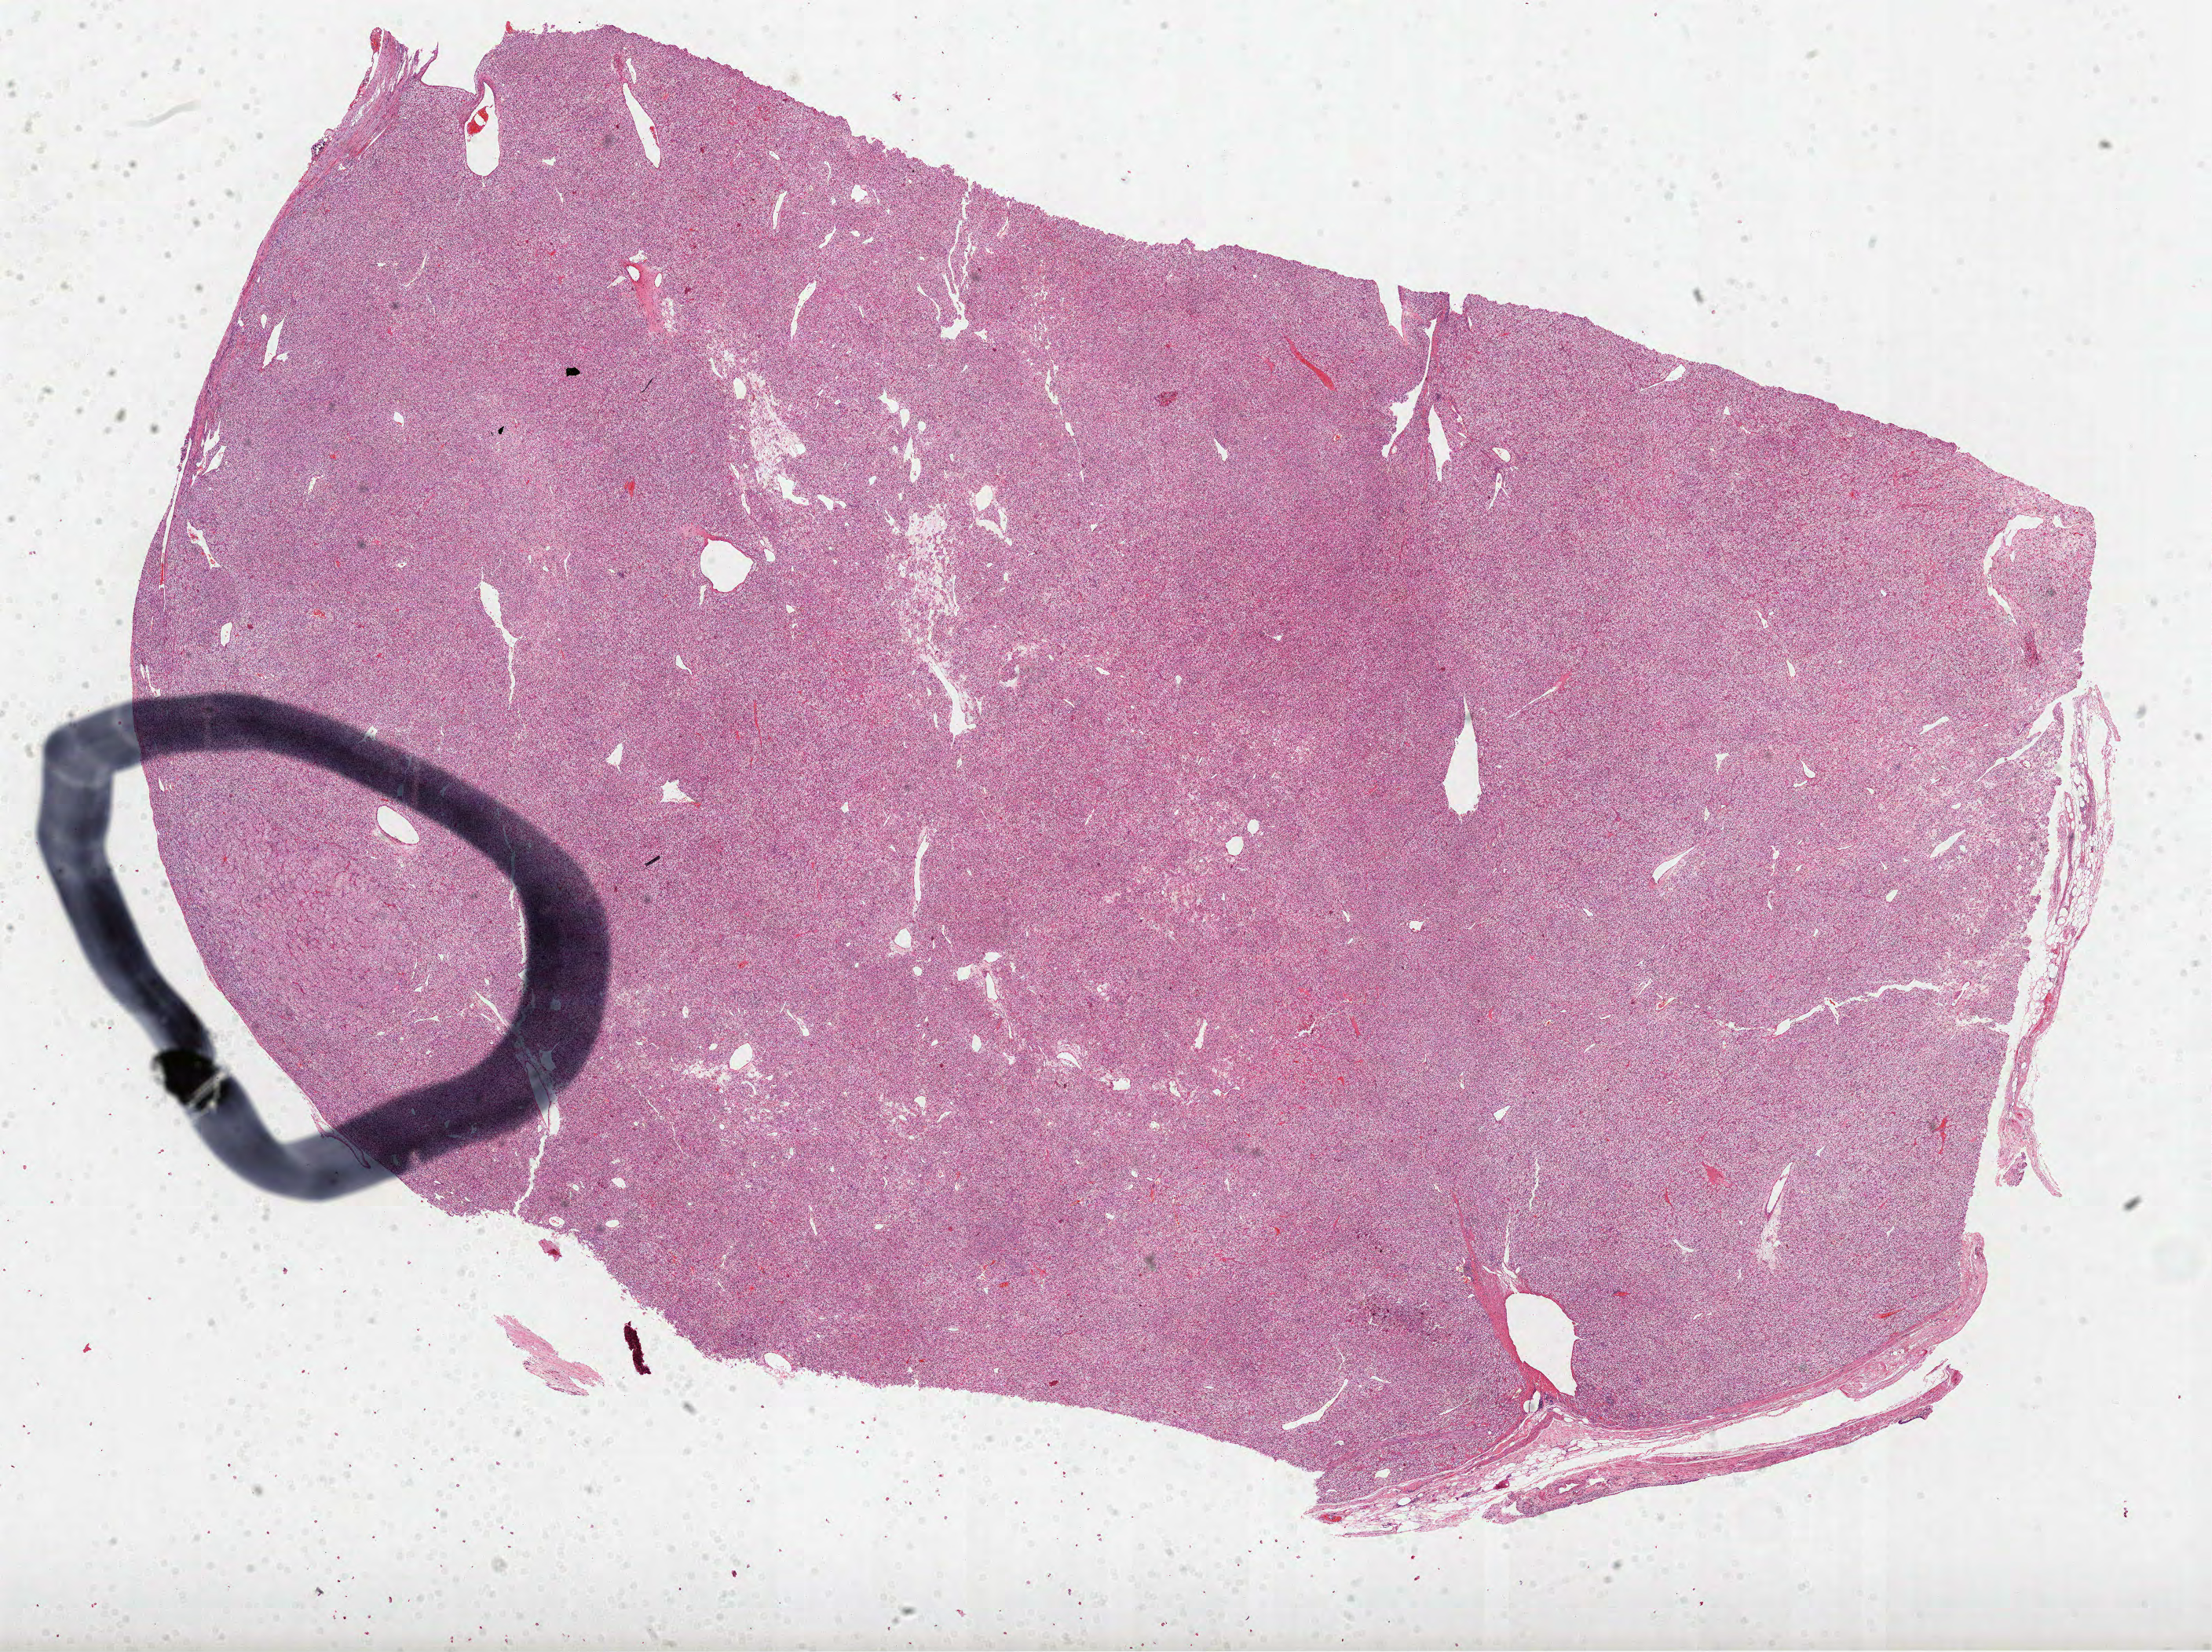
Whole-slide histology image, H&E, whole scanned area (about 22.7 x 17.0 mm, acquisition: 40x scan) shown as a low-resolution overview; formalin-fixed paraffin-embedded (FFPE) diagnostic section; kidney, primary tumour sample. Male, age 81 years at initial diagnosis. Histologic grade: G3 (poorly differentiated).
AJCC pathologic stage: IV. Lymph nodes positive (case pathology): 0 of 1 examined. Histologic diagnosis: Clear cell adenocarcinoma, NOS.